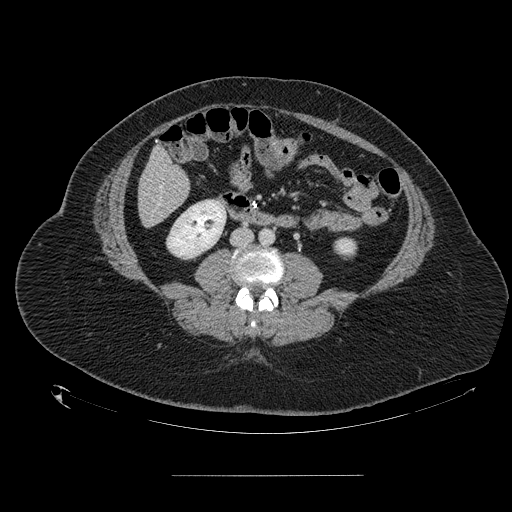
Contrast-enhanced abdominal CT, one axial slice; slice 30 of 164 in the series (ordered by position); 120 kVp; intravenous contrast given; soft-tissue window (W 400 / L 40 HU); 2.5 mm slice thickness; 512 × 512 image matrix, field of view 495 × 495 mm. Female patient, age 52 years. From the clinical record (not read from this slice): diagnosis: colorectal cancer liver metastases, imaged before liver resection; multiple liver metastases: yes; largest metastasis: 3.5 cm; disease in both lobes: no.
Outlined on this slice (manually delineated by an expert):
- hepatic veins: box from (x=160, y=186) to (x=162, y=188) px
- liver: (x=140, y=149)–(x=190, y=227)